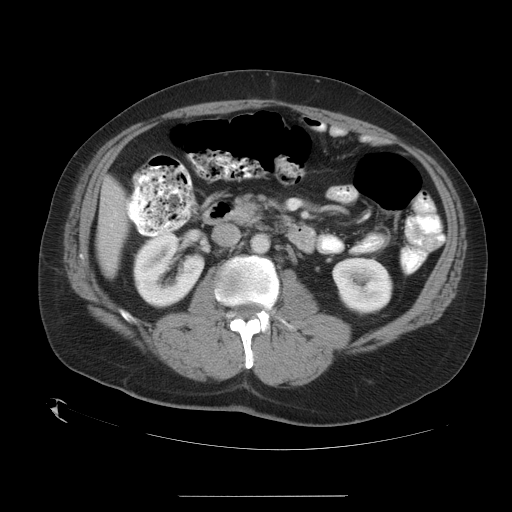
Contrast-enhanced abdominal CT, one axial slice; slice 10 of 35 in the series (ordered by position); reconstruction kernel STANDARD; 120 kVp; intravenous contrast given; soft-tissue window (W 400 / L 40 HU); 7.5 mm slice thickness; 512 × 512 image matrix, field of view 450 × 450 mm. Male patient, age 67 years. From the clinical record (not read from this slice): diagnosis: colorectal cancer liver metastases, imaged before liver resection; multiple liver metastases: no; largest metastasis: 2.3 cm; chemotherapy before resection: no.
Annotated regions visible in this slice (outlined manually by an expert reader):
- liver: bounding box <98,182,126,270> (left, top, right, bottom; pixels)
- planned liver remnant (the part of the liver to remain after resection): <98,182,126,270>
- portal vein (with intrahepatic branches): <111,204,129,226>